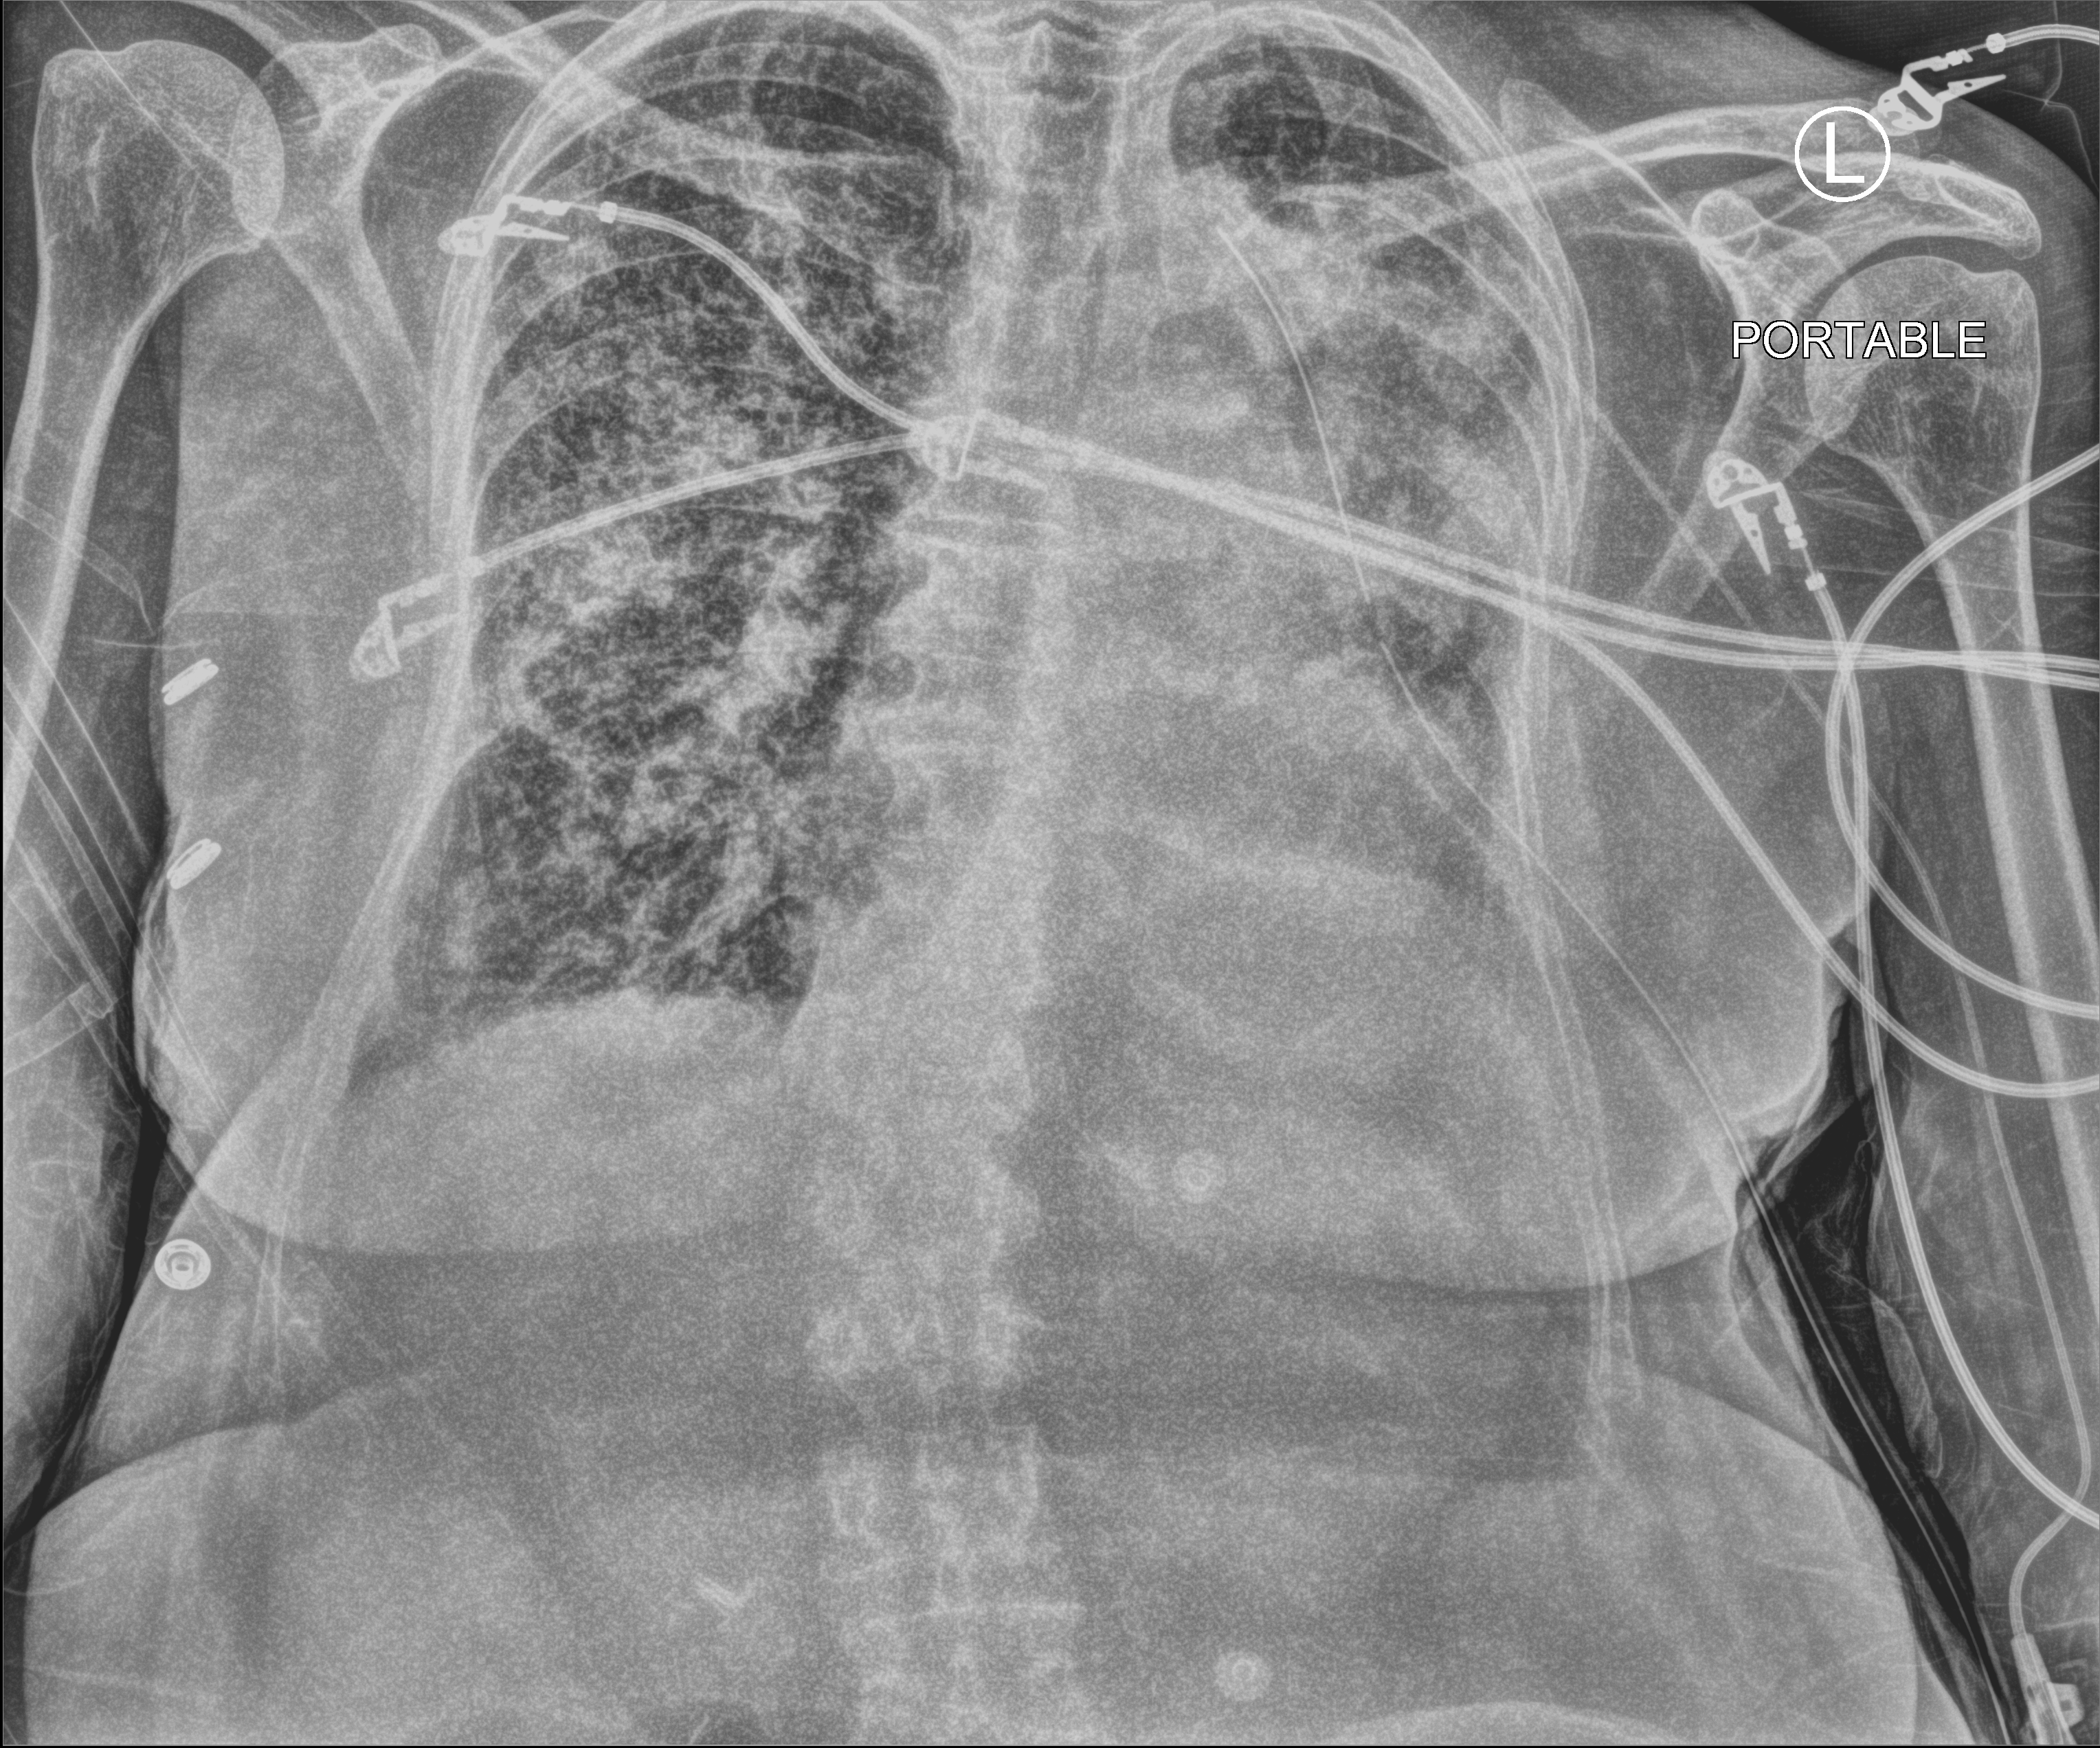
Chest X-ray (portable), anteroposterior (AP) projection. Female patient hospitalised with COVID-19, age 75–90 years.
From the hospital-stay record, not from the radiograph (when in the stay this image was taken is not recorded):
- admitted to intensive care during this hospital stay: yes
- length of hospital stay: 70 days
- mechanically ventilated during this hospital stay: yes